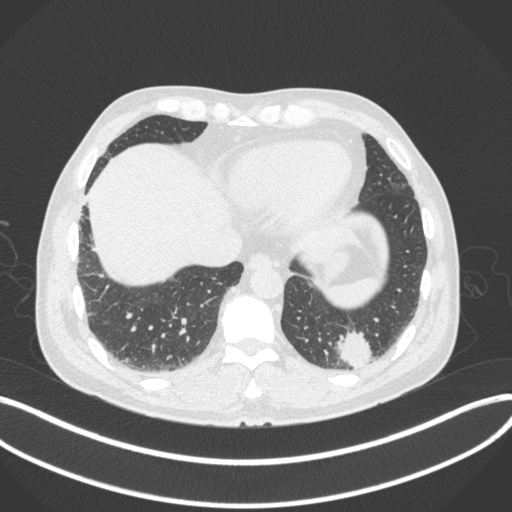
Chest CT, one axial slice; slice 63 of 313 in the series (ordered by position); 120 kVp; lung window (W 1500 / L -600 HU); 1 mm slice thickness; 512 × 512 image matrix. Patient: male, 54 years. Case-level facts recorded for this patient, not image findings: clinical TNM (as recorded): T1c N0 M1; histopathological grade: G3.
Structures marked on this image (rectangle marked by the reading radiologist):
- lung tumour (recorded histology: adenocarcinoma): box from (x=331, y=328) to (x=377, y=373) px